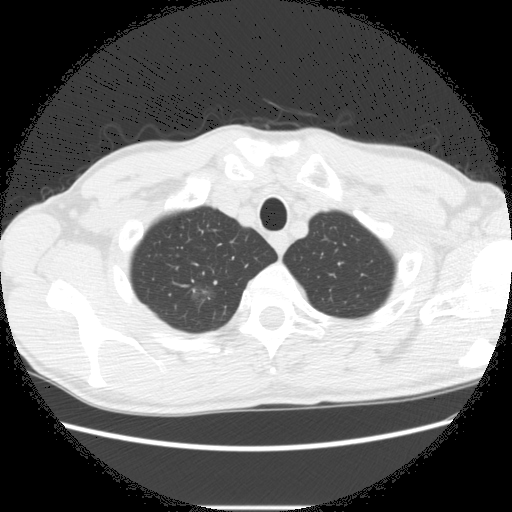
Low-dose screening chest CT, one axial slice. Position 252 of 282 along the scan axis. 120 kVp. Lung window (W 1500 / L -600 HU). 2.5 mm slice thickness. 512 × 512 image matrix, field of view 360 × 360 mm.
Structures marked on this image (manually delineated by an expert):
- lesion 2 (nodule, upper lobe of right lung): bounding box <190,285,215,302> (left, top, right, bottom; pixels)